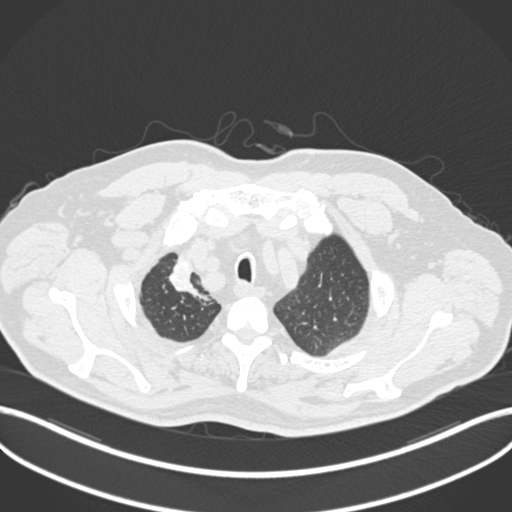
Chest CT, one axial slice. Reconstruction kernel B30f. 120 kVp. Lung window (W 1500 / L -600 HU). 512 × 512 image matrix. Male patient, age 60 years. From the clinical record (not read from this slice): clinical TNM (as recorded): T1b N1 M0.
Annotated regions visible in this slice (rectangle marked by the reading radiologist):
- lung tumour (recorded histology: squamous cell carcinoma): bounding box [x1, y1, x2, y2] px = [166, 254, 211, 308]